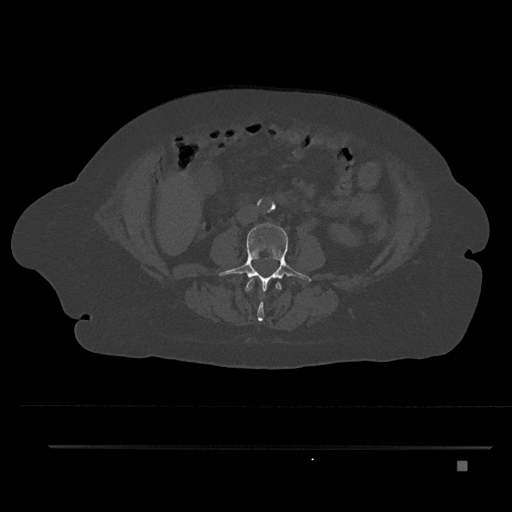
CT including the spine, one axial slice; slice 131 of 797 in the series (ordered by position); 120 kVp; bone window (W 1800 / L 400 HU); 0.5 mm slice thickness; 512 × 512 image matrix, field of view 437 × 437 mm. Female patient, age 76 years. Case-level facts recorded for this patient, not image findings: primary cancer: lung.
Outlined on this slice (semi-automatically segmented with operator editing):
- L2 vertebra: bounding box <245,279,282,322> (left, top, right, bottom; pixels)
- L3 vertebra: <218,223,311,292>